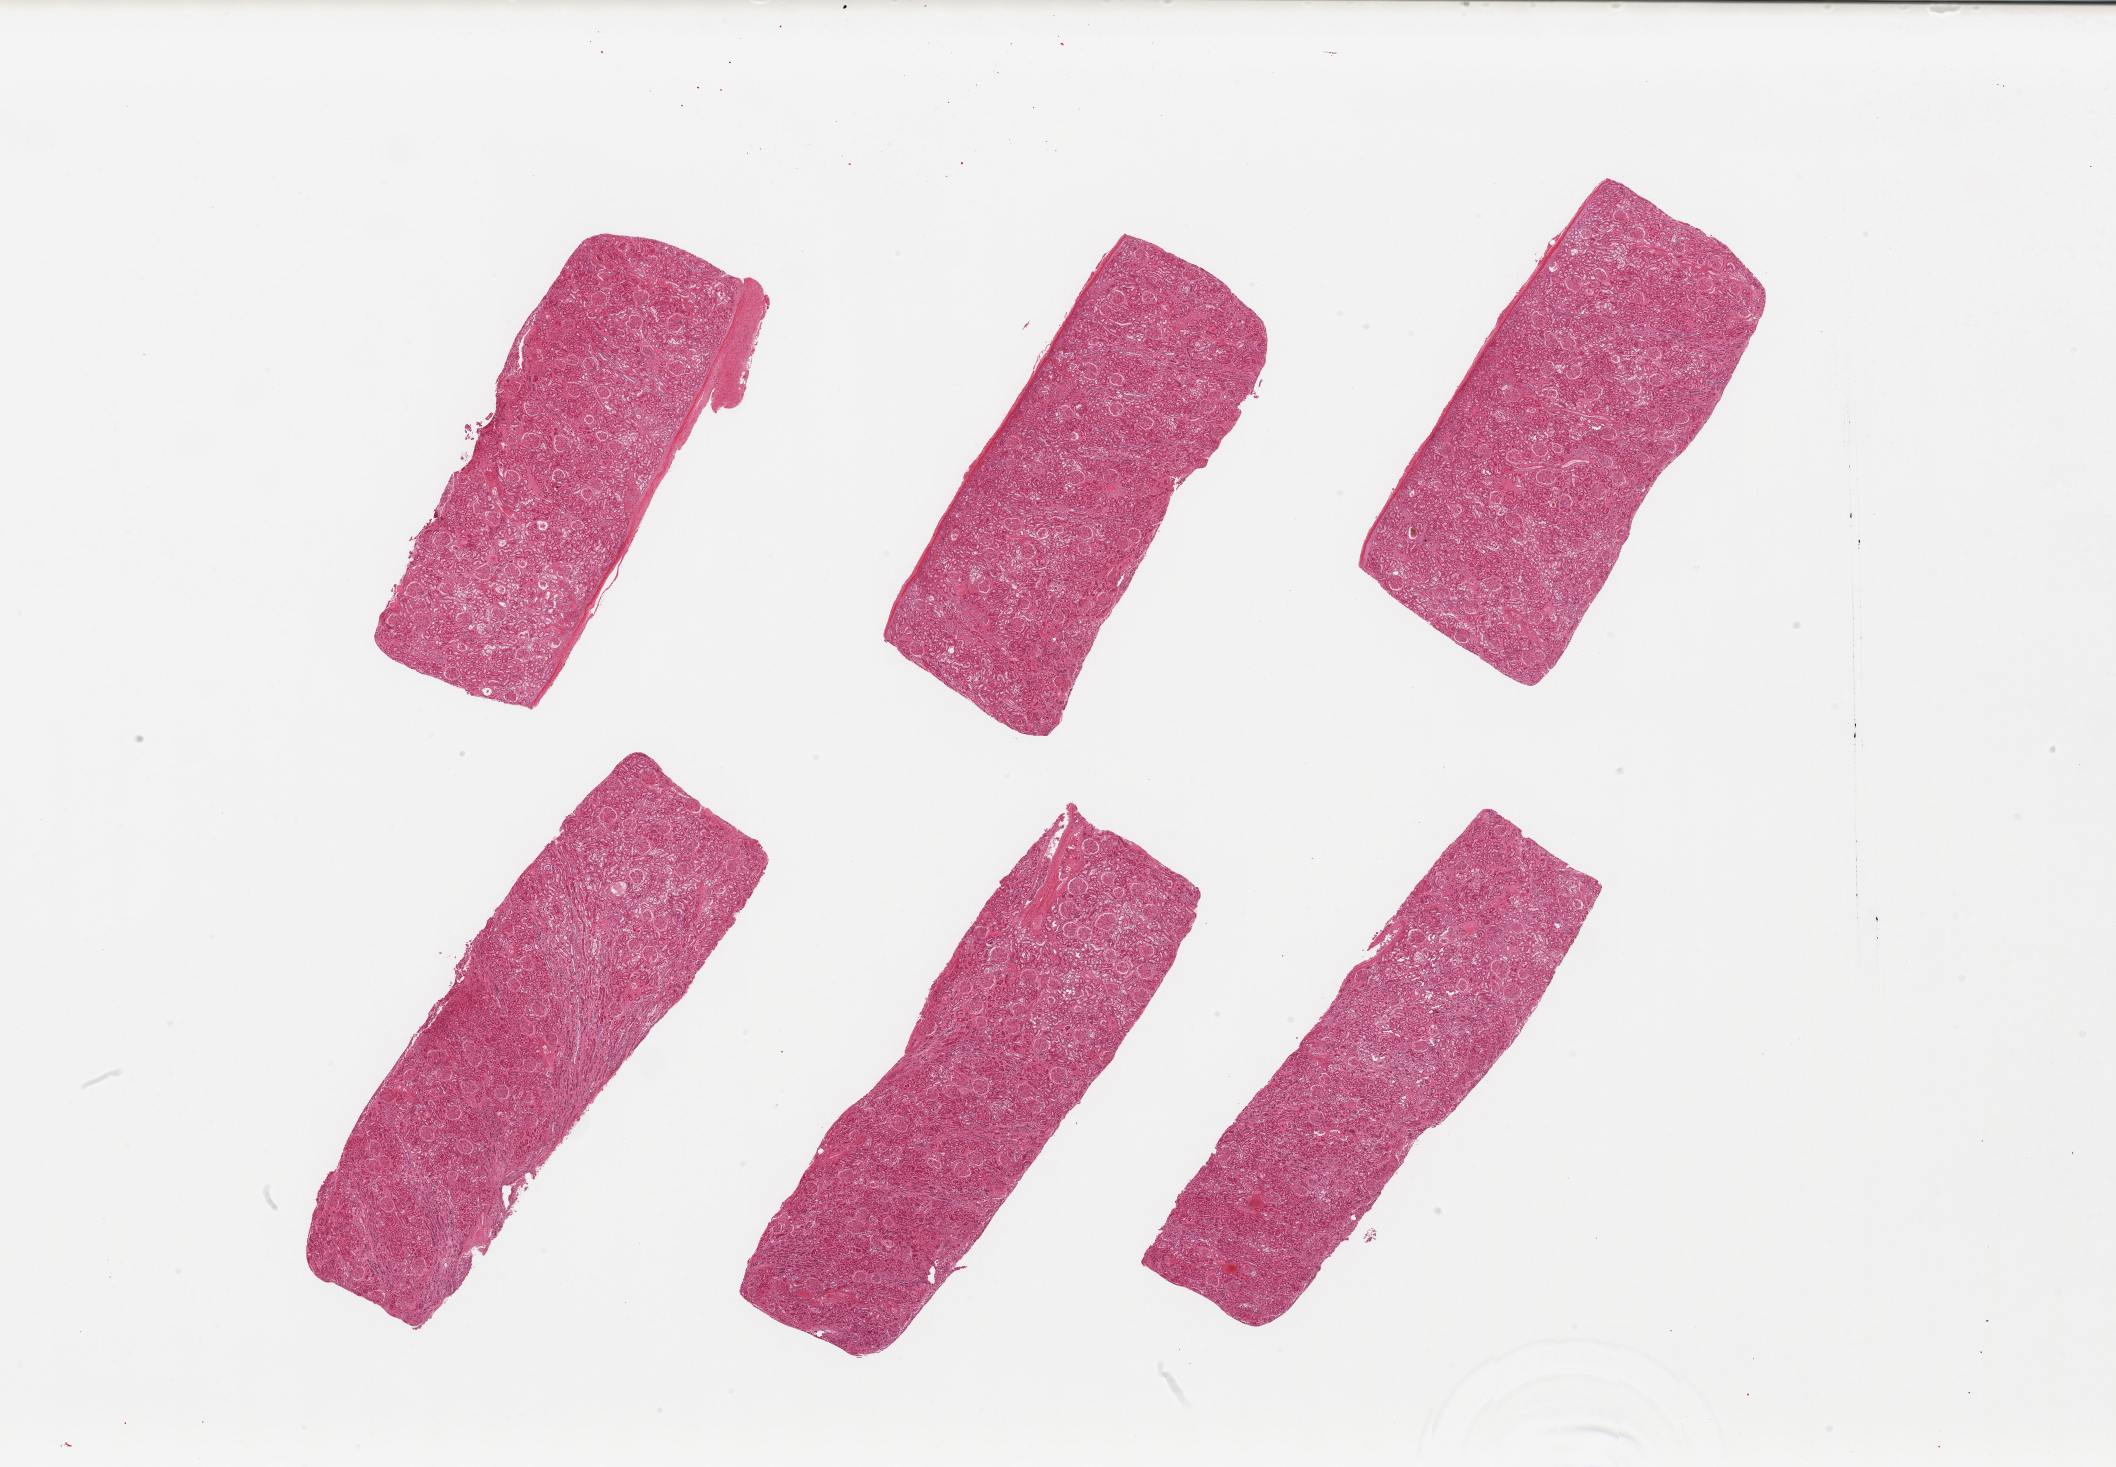
Digitized haematoxylin and eosin-stained section — a low-resolution overview of the entire scanned area, about 33.5 x 23.2 mm (from a 20x scan); PAXgene-fixed paraffin-embedded (PFPE) section; sampled site (target tissue): renal cortex; tissue donor sample. Male donor.
Pathologist's review note for this sample: 6 pieces, glomeruli present, tubules with moderated advanced autolysis.